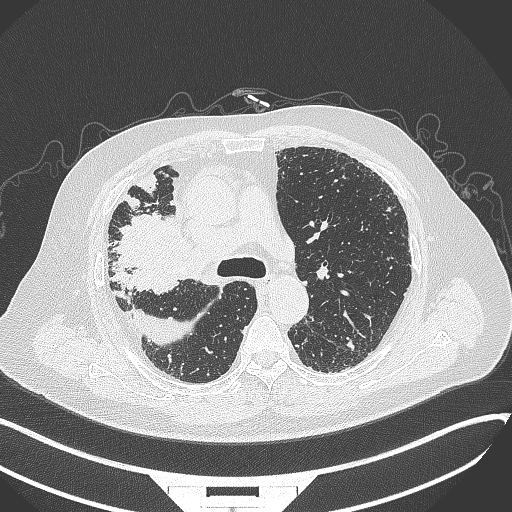
Chest CT, one axial slice. Position 228 of 384 along the scan axis. 120 kVp. Lung window (W 1500 / L -600 HU). 1 mm slice thickness. 512 × 512 image matrix, field of view 400 × 400 mm. Male patient, age 69 years. From the clinical record (not read from this slice): clinical TNM (as recorded): T4 N3 M1.
Outlined on this slice (rectangle marked by the reading radiologist):
- lung tumour (recorded histology: adenocarcinoma): bounding box [x1, y1, x2, y2] px = [108, 209, 192, 298]